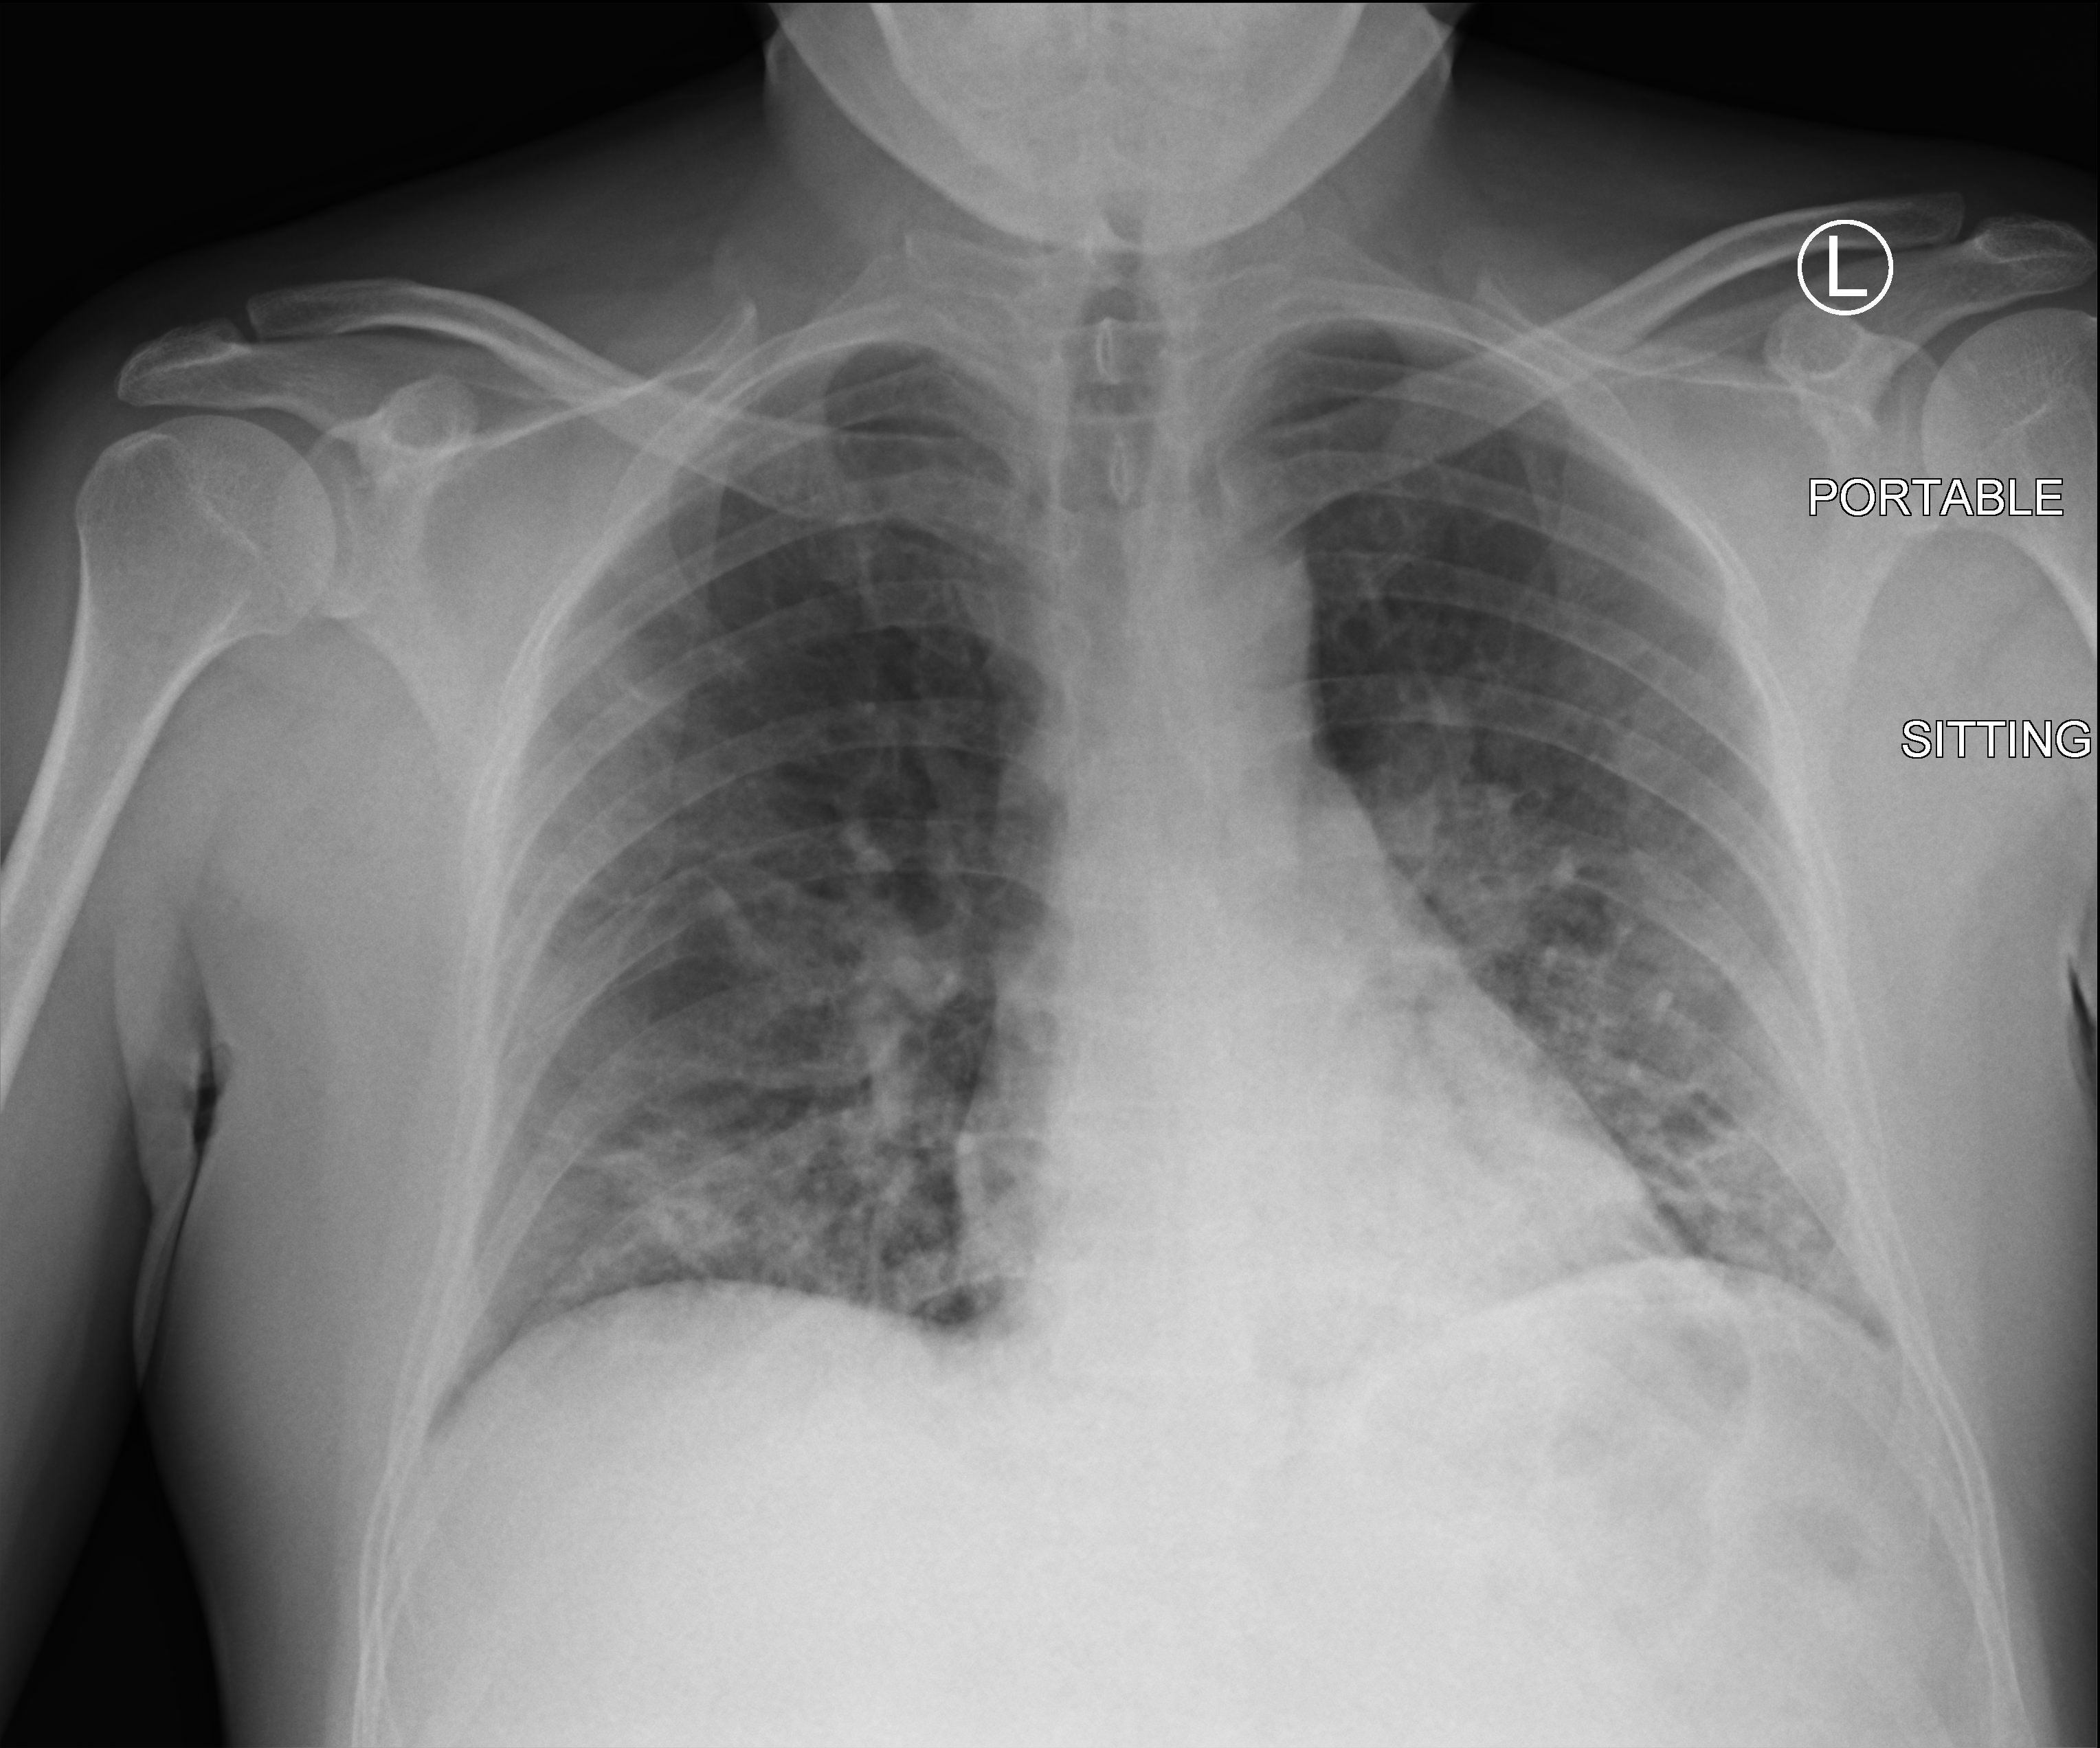
Bedside chest radiograph (computed radiography); anteroposterior (AP) projection. Patient hospitalised with COVID-19; male, aged 18–59 years.
Hospital-stay facts (about this admission, not read from this image; timing relative to this image not recorded):
- admitted to intensive care during this hospital stay: no